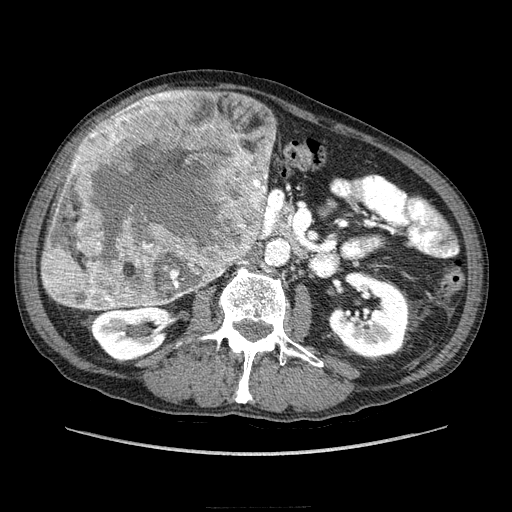
Contrast-enhanced abdominal CT (liver protocol), one axial slice. Slice 87 of 218 in the series (ordered by position). Reconstruction kernel STANDARD. 100 kVp. Soft-tissue window (W 400 / L 40 HU). 512 × 512 image matrix. Case-level facts recorded for this patient, not image findings: diagnosis: hepatocellular carcinoma (patient treated with transarterial chemoembolisation; whether this scan precedes or follows treatment is not stated here); TNM stage (as recorded): Stage-IIIA; Child-Pugh class: A; tumour nodularity: multinodular.
Structures marked on this image (semi-automatic segmentation, software-assisted and operator-edited):
- liver parenchyma outside the tumour (the mass and vessels are separate outlines, so this box may not span the whole liver): bounding box <70,120,276,183> (left, top, right, bottom; pixels)
- mass: <40,89,275,312>